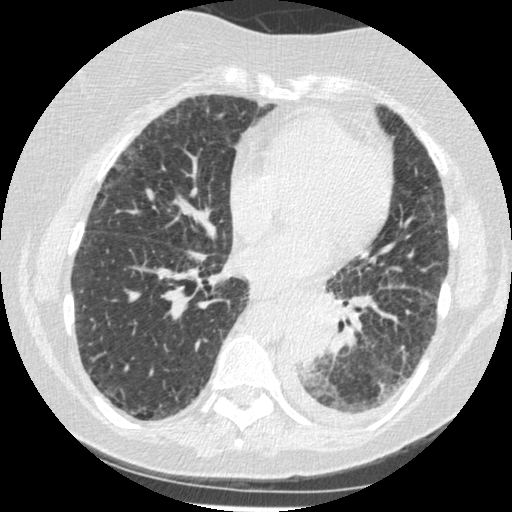
Chest CT (low-dose screening protocol), one axial image, third screening round (two years after baseline), lung window (W 1500 / L -600 HU), 1.25 mm slice thickness, standard (soft-tissue) reconstruction kernel (STANDARD), slice 247 of 341 in the series, 512 × 512 image matrix. Female, age 60 years at enrolment. Former smoker at enrolment.
Expert reader's lesion annotation, bounding box [x1, y1, x2, y2] px = [277, 302, 343, 376]. Screening reader's record for this exam (one nodule recorded; not confirmed to be the boxed lesion): non-calcified nodule or mass ≥4 mm, left lower lobe, 54 × 38 mm, smooth margins, soft tissue attenuation, pre-existing on the prior screen: yes; interval growth: yes. Official screen result: positive, other.